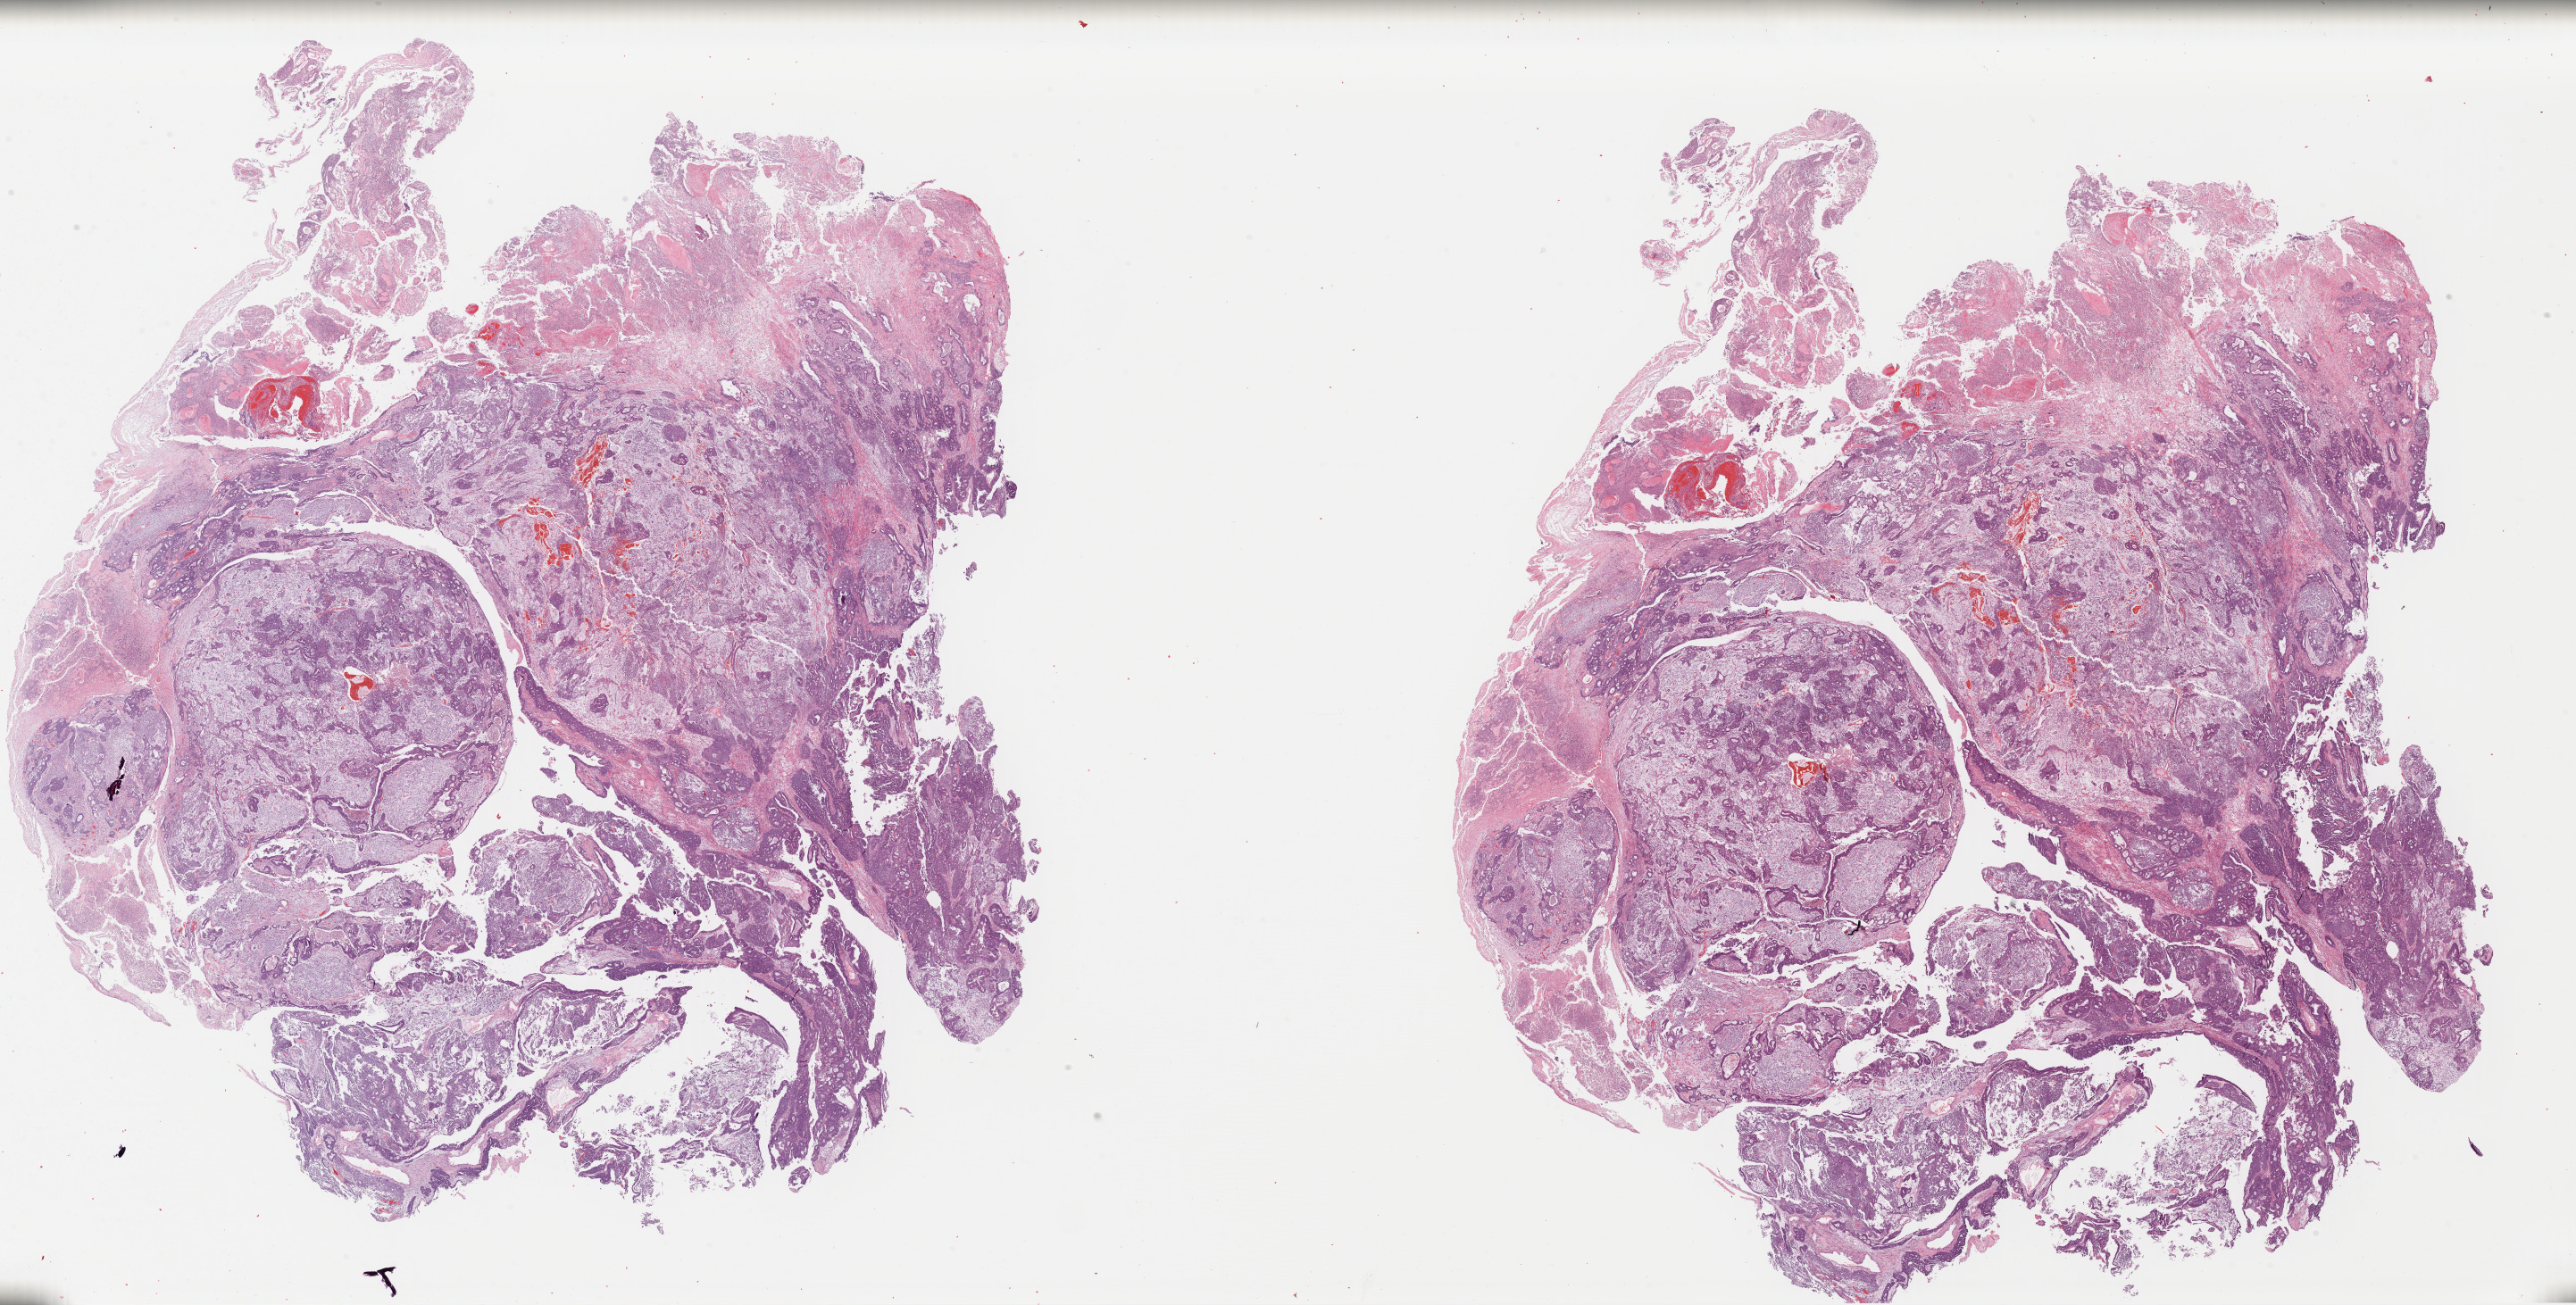
Whole-slide histology image, Hematoxylin and eosin (H&E) stained, low-resolution overview of the scanned area, about 45.4 x 23.0 mm, formalin-fixed paraffin-embedded (FFPE) diagnostic section, uterus, primary tumour sample. Female patient; age at initial diagnosis 74 years.
FIGO stage: IC. Histologic diagnosis: Mullerian mixed tumor (endometrium).